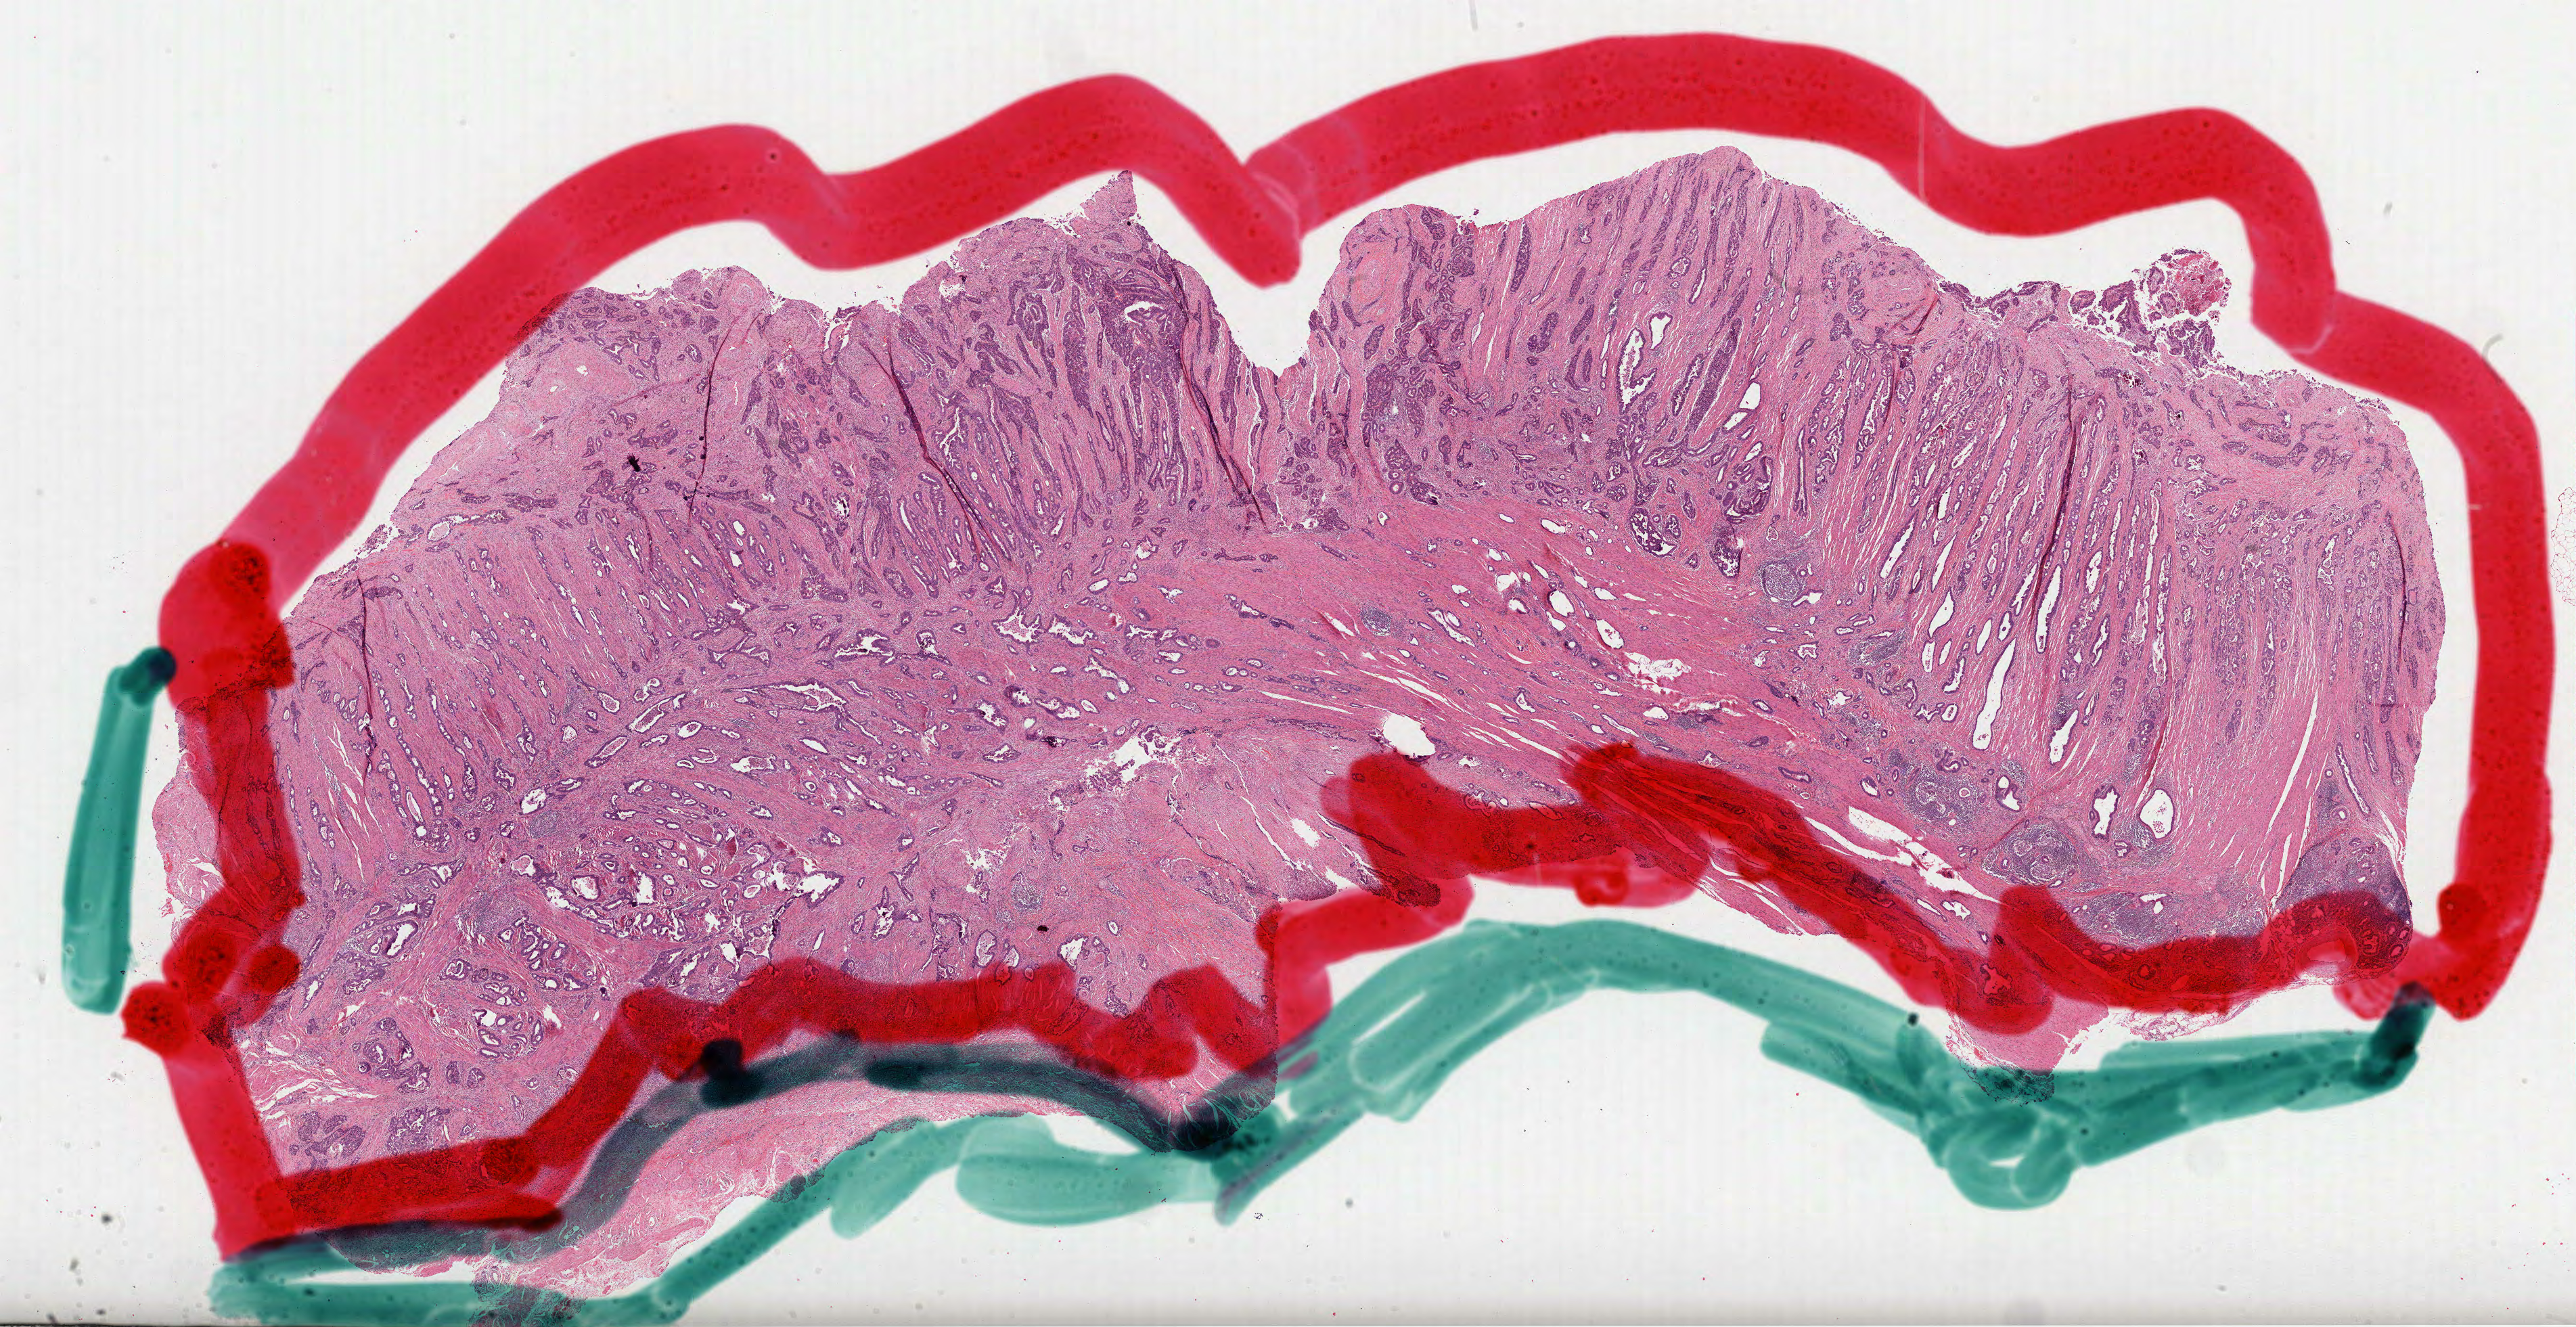
Whole-slide histology image, Hematoxylin and eosin (H&E) stained — a low-resolution overview of the entire scanned area, about 30.7 x 15.8 mm (slide scanned at 40x), FFPE section, sample: primary tumour, rectum. Patient: male, age at initial diagnosis 67 years.
AJCC pathologic stage: IIA (7th edition). Diagnosis: Adenocarcinoma, NOS (connective, subcutaneous and other soft tissues of abdomen). TNM: T3 N0 M0.